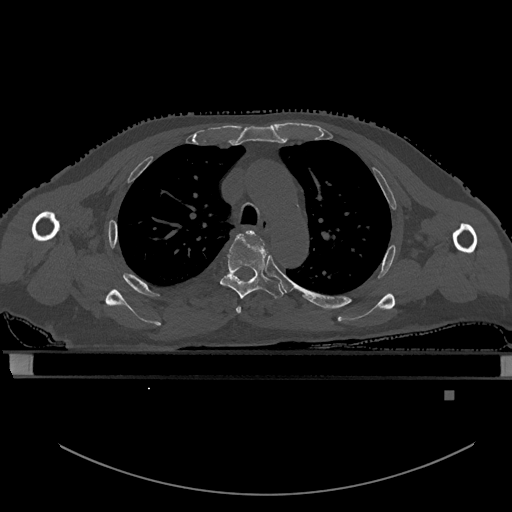
CT including the spine, one axial slice; position 410 of 969 along the scan axis; bone window (W 1800 / L 400 HU); 0.5 mm slice thickness; 512 × 512 image matrix, field of view 456 × 456 mm. Male patient, age 82 years. Case-level facts recorded for this patient, not image findings: primary cancer: prostate.
Outlined on this slice (semi-automatically segmented with operator editing):
- T3 vertebra: bounding box (x1, y1, x2, y2) in pixels: (236, 230, 254, 314)
- T4 vertebra: (220, 235, 283, 299)